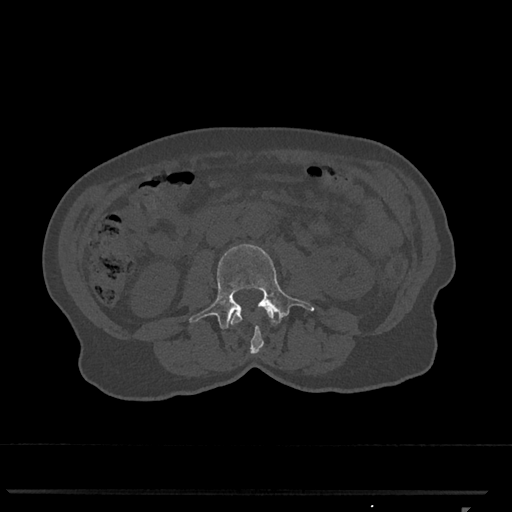
CT including the spine, one axial slice. Slice 288 of 793 in the series (ordered by position). Bone window (W 1800 / L 400 HU). 0.5 mm slice thickness. 512 × 512 image matrix. Female patient, age 62 years. From the clinical record (not read from this slice): primary cancer: renal.
Outlined on this slice (semi-automatic segmentation, software-assisted and operator-edited):
- L2 vertebra: bounding box [x1, y1, x2, y2] px = [229, 307, 279, 354]
- L3 vertebra: [189, 244, 315, 329]